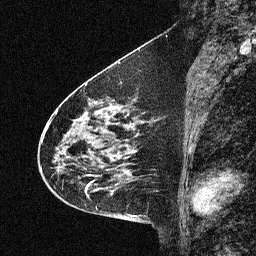
Breast MRI (dynamic contrast-enhanced), one sagittal slice. Position 25 of 64 along the scan axis. Dynamic contrast-enhanced study with each time point stored as its own series, time point 2 of 3 at this slice position (early post-contrast, ordered by acquisition time). 1.5 T. TE 4.5 ms, TR 11 ms. 2.06 mm slice thickness. 256 × 256 image matrix. Patient: female, 46 years. Case-level facts recorded for this patient, not image findings: setting: breast cancer imaged before/during neoadjuvant chemotherapy; receptor status: HER2-positive.
Annotated regions visible in this slice (semi-automatic segmentation, software-assisted and operator-edited):
- analysis volume of interest (the breast-tissue region the enhancement analysis was run in; not a lesion): box from (x=42, y=80) to (x=150, y=180) px
- tumour enhancement mask (voxels above the 90 % enhancement threshold inside the analysis volume of interest): (x=55, y=84)–(x=128, y=177)